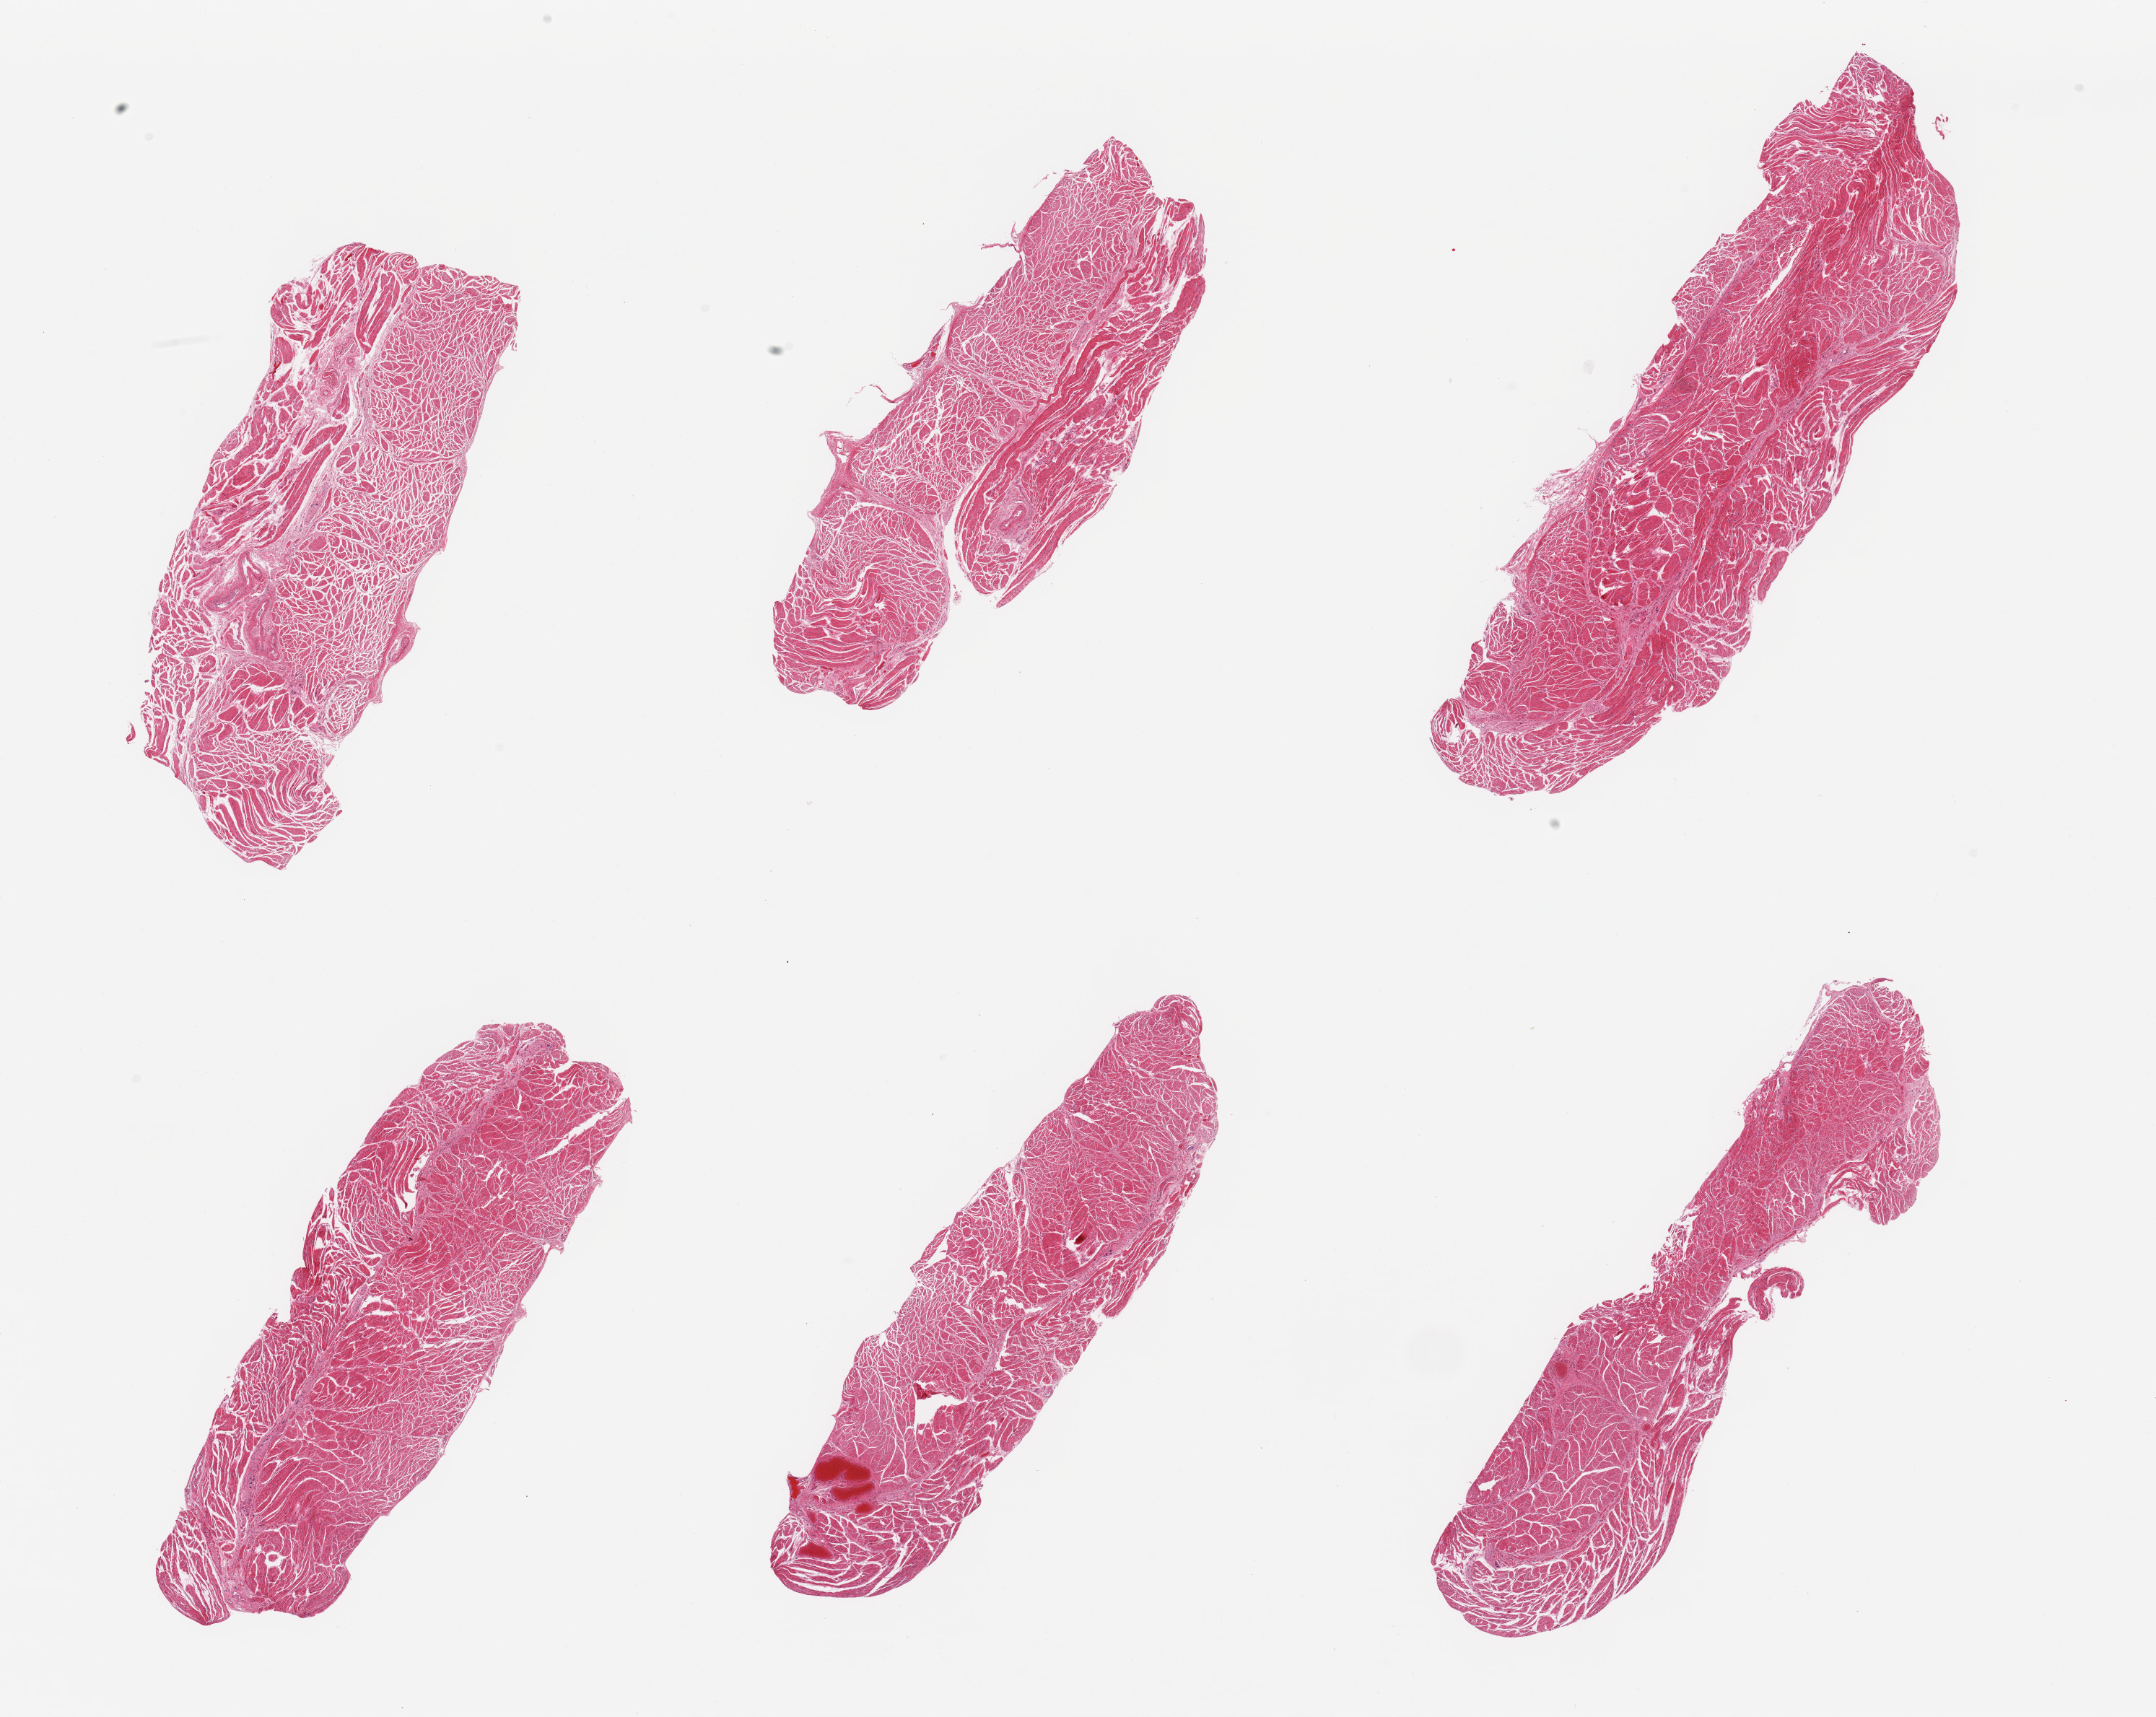
Haematoxylin and eosin whole-slide image — low-resolution overview of the scanned area, about 23.6 x 18.8 mm. PAXgene-fixed paraffin-embedded (PFPE) section. Target tissue: esophageal muscle. Donor tissue sample.
Reviewer comment on this tissue sample: 6 pieces, confirmed target muscularis.